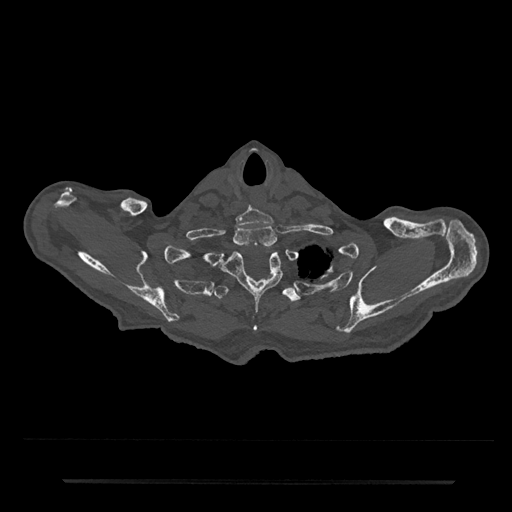
CT including the spine, one axial slice. Position 697 of 797 along the scan axis. Reconstruction kernel Br40s/3. 120 kVp. Bone window (W 1800 / L 400 HU). 0.5 mm slice thickness. 512 × 512 image matrix, field of view 427 × 427 mm. Male patient, age 74 years. From the clinical record (not read from this slice): primary cancer: prostate.
Structures marked on this image (semi-automatically segmented with operator editing):
- T1 vertebra: bounding box <234,225,277,249> (left, top, right, bottom; pixels)
- T2 vertebra: <218,251,283,330>
- T3 vertebra: <214,285,301,302>